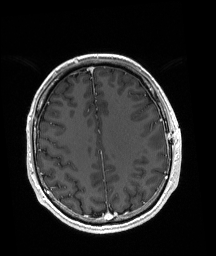
Brain MRI from a brain-tumour surgery series, one axial slice; slice 65 of 192 in the series (ordered by position); T1-weighted post-contrast; 1 mm slice thickness; 216 × 256 image matrix. Case-level facts recorded for this patient, not image findings: histopathology: Astrocytoma; WHO grade: 3; IDH mutation: yes.
Annotated regions visible in this slice (manually delineated by an expert):
- tumour: box from (x=149, y=132) to (x=163, y=148) px